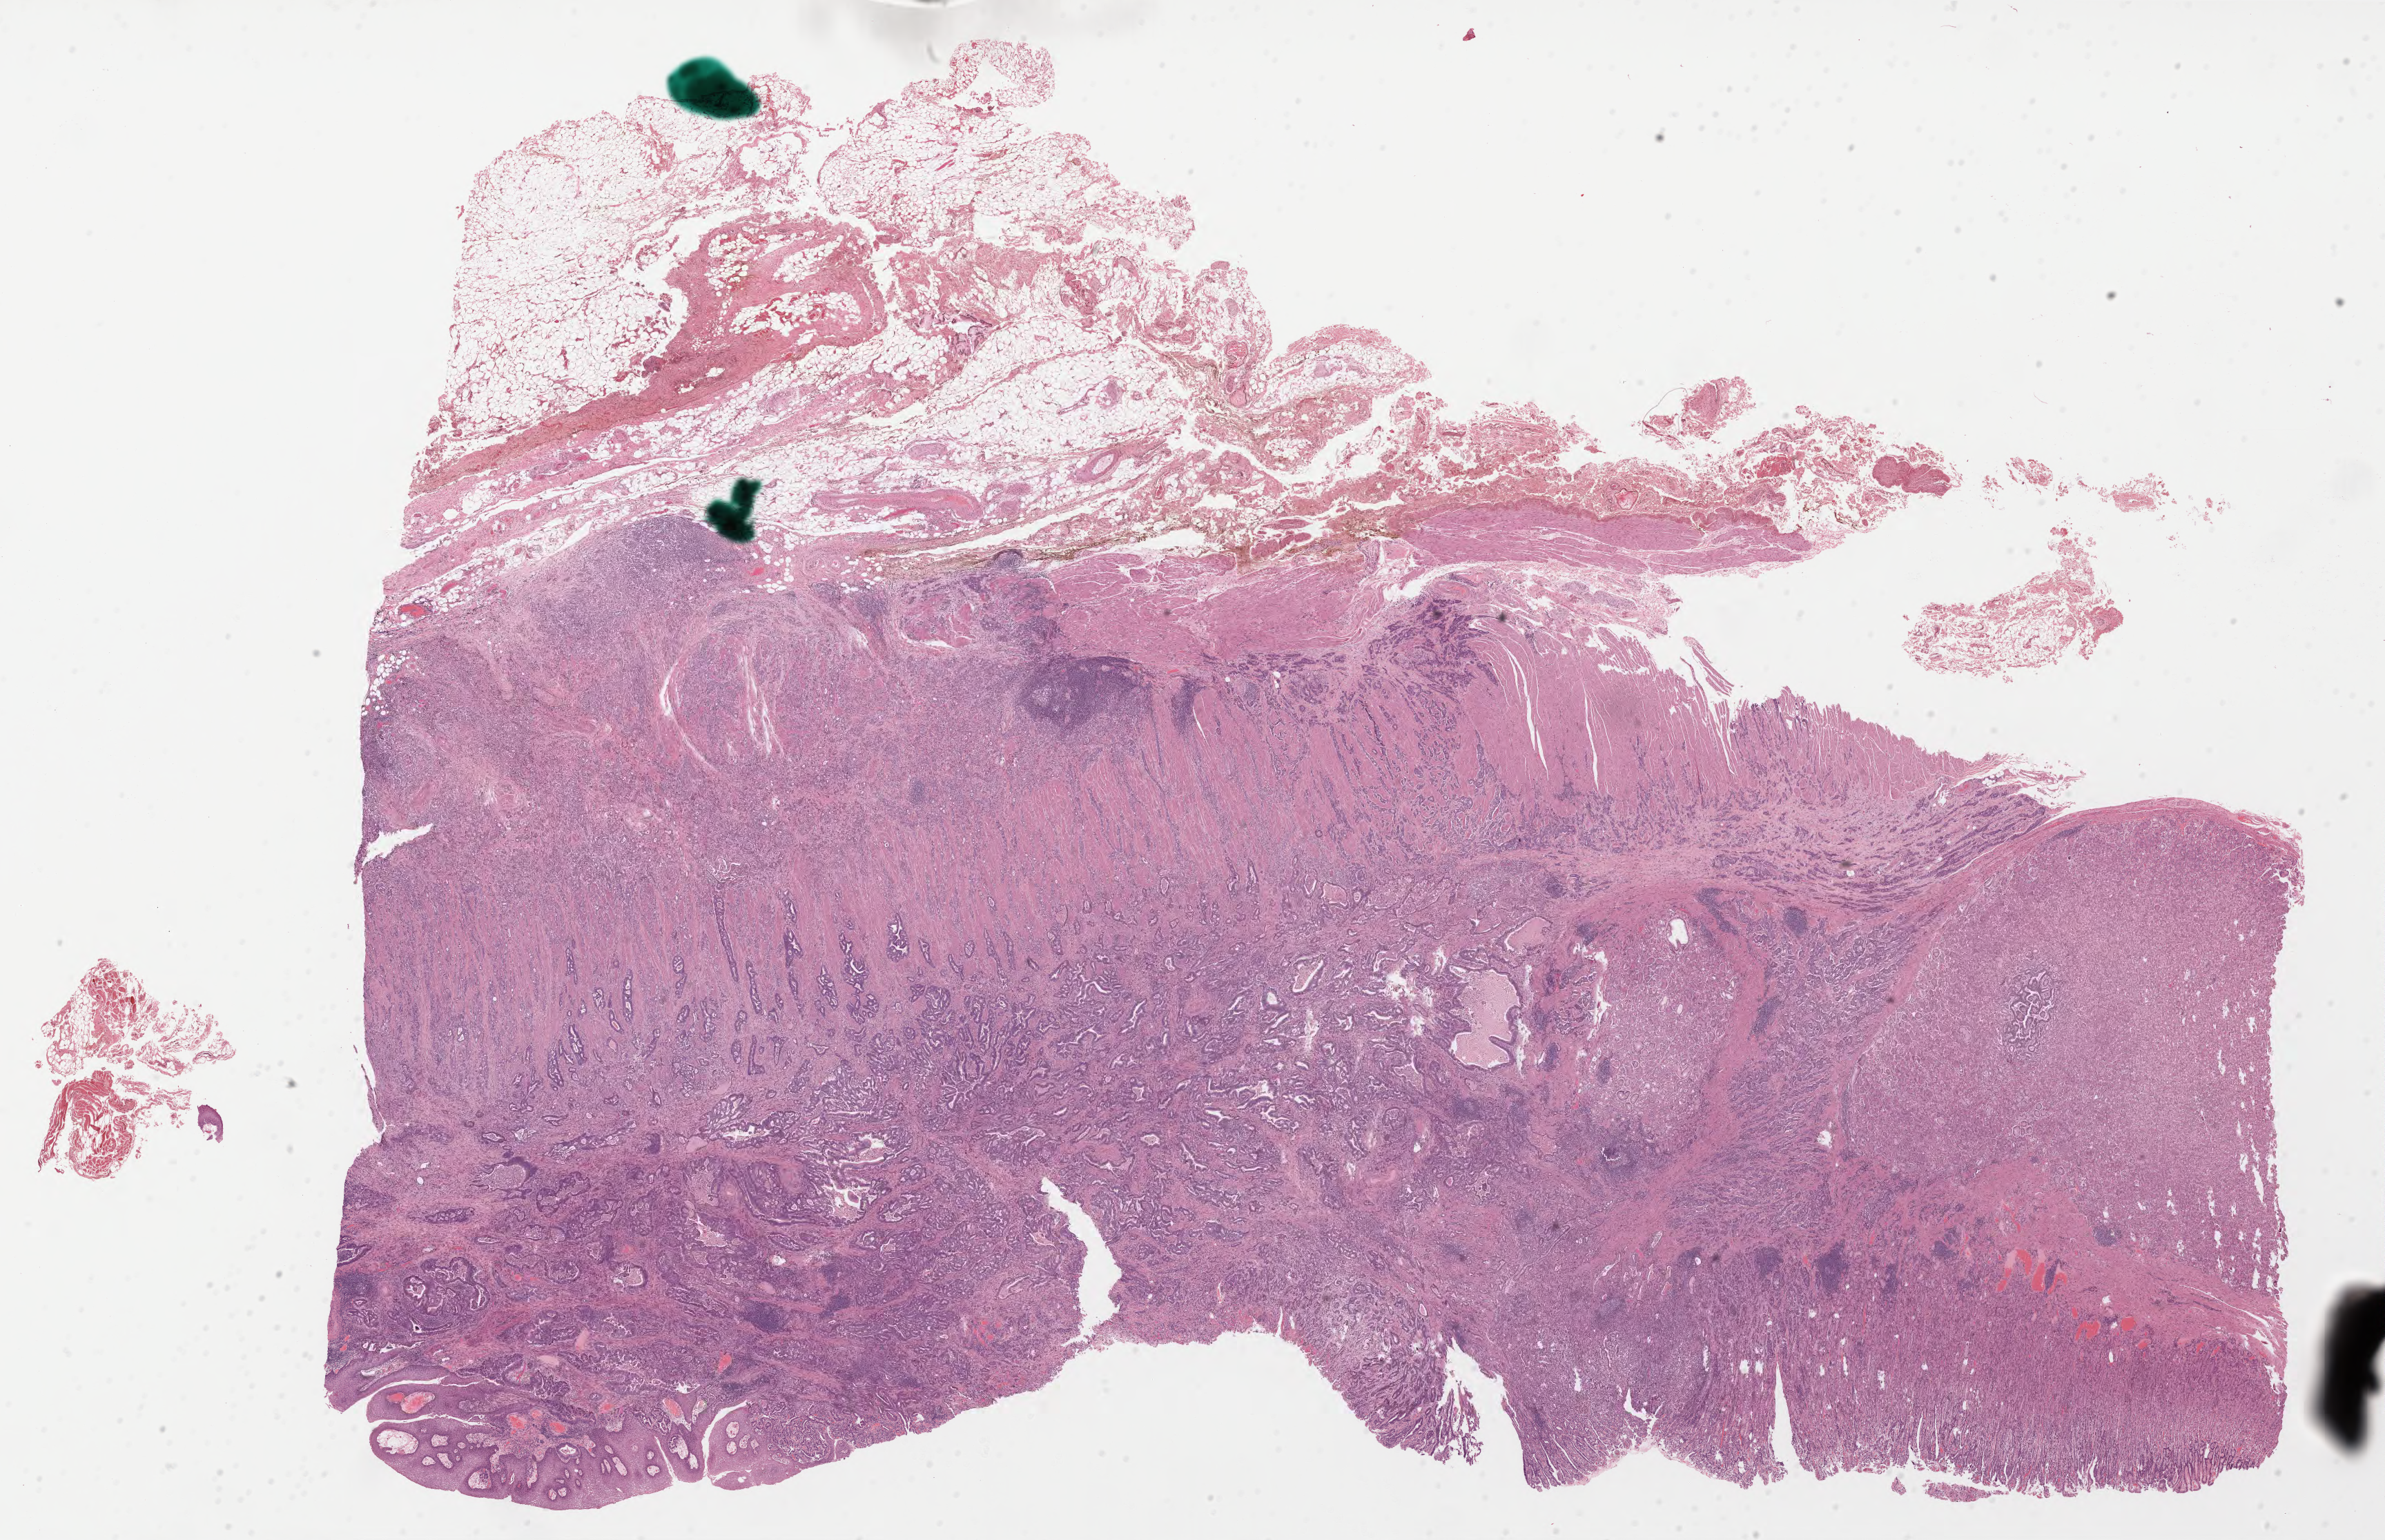
Whole-slide histology image, H&E-stained, shown as a low-resolution overview of the whole scanned area (about 27.8 x 18.0 mm, acquisition: 40x scan). Formalin-fixed paraffin-embedded (FFPE) diagnostic section. Esophagus, primary tumour sample. Male, age 61 years at initial diagnosis. Histologic grade: G3 (poorly differentiated).
Diagnosis: Adenocarcinoma, NOS. AJCC pathologic stage: IIIA (7th edition).